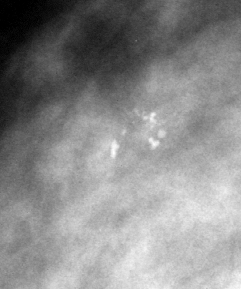
Cropped region of a digitized screen-film mammogram centred on a radiologist-marked abnormality, right breast, MLO view.
- Marked abnormality: calcifications, morphology pleomorphic, distribution clustered; BI-RADS assessment category 4; subtlety rating 4 on a 1 (subtle) to 5 (obvious) scale; pathology result (as recorded, not read from the image): benign.